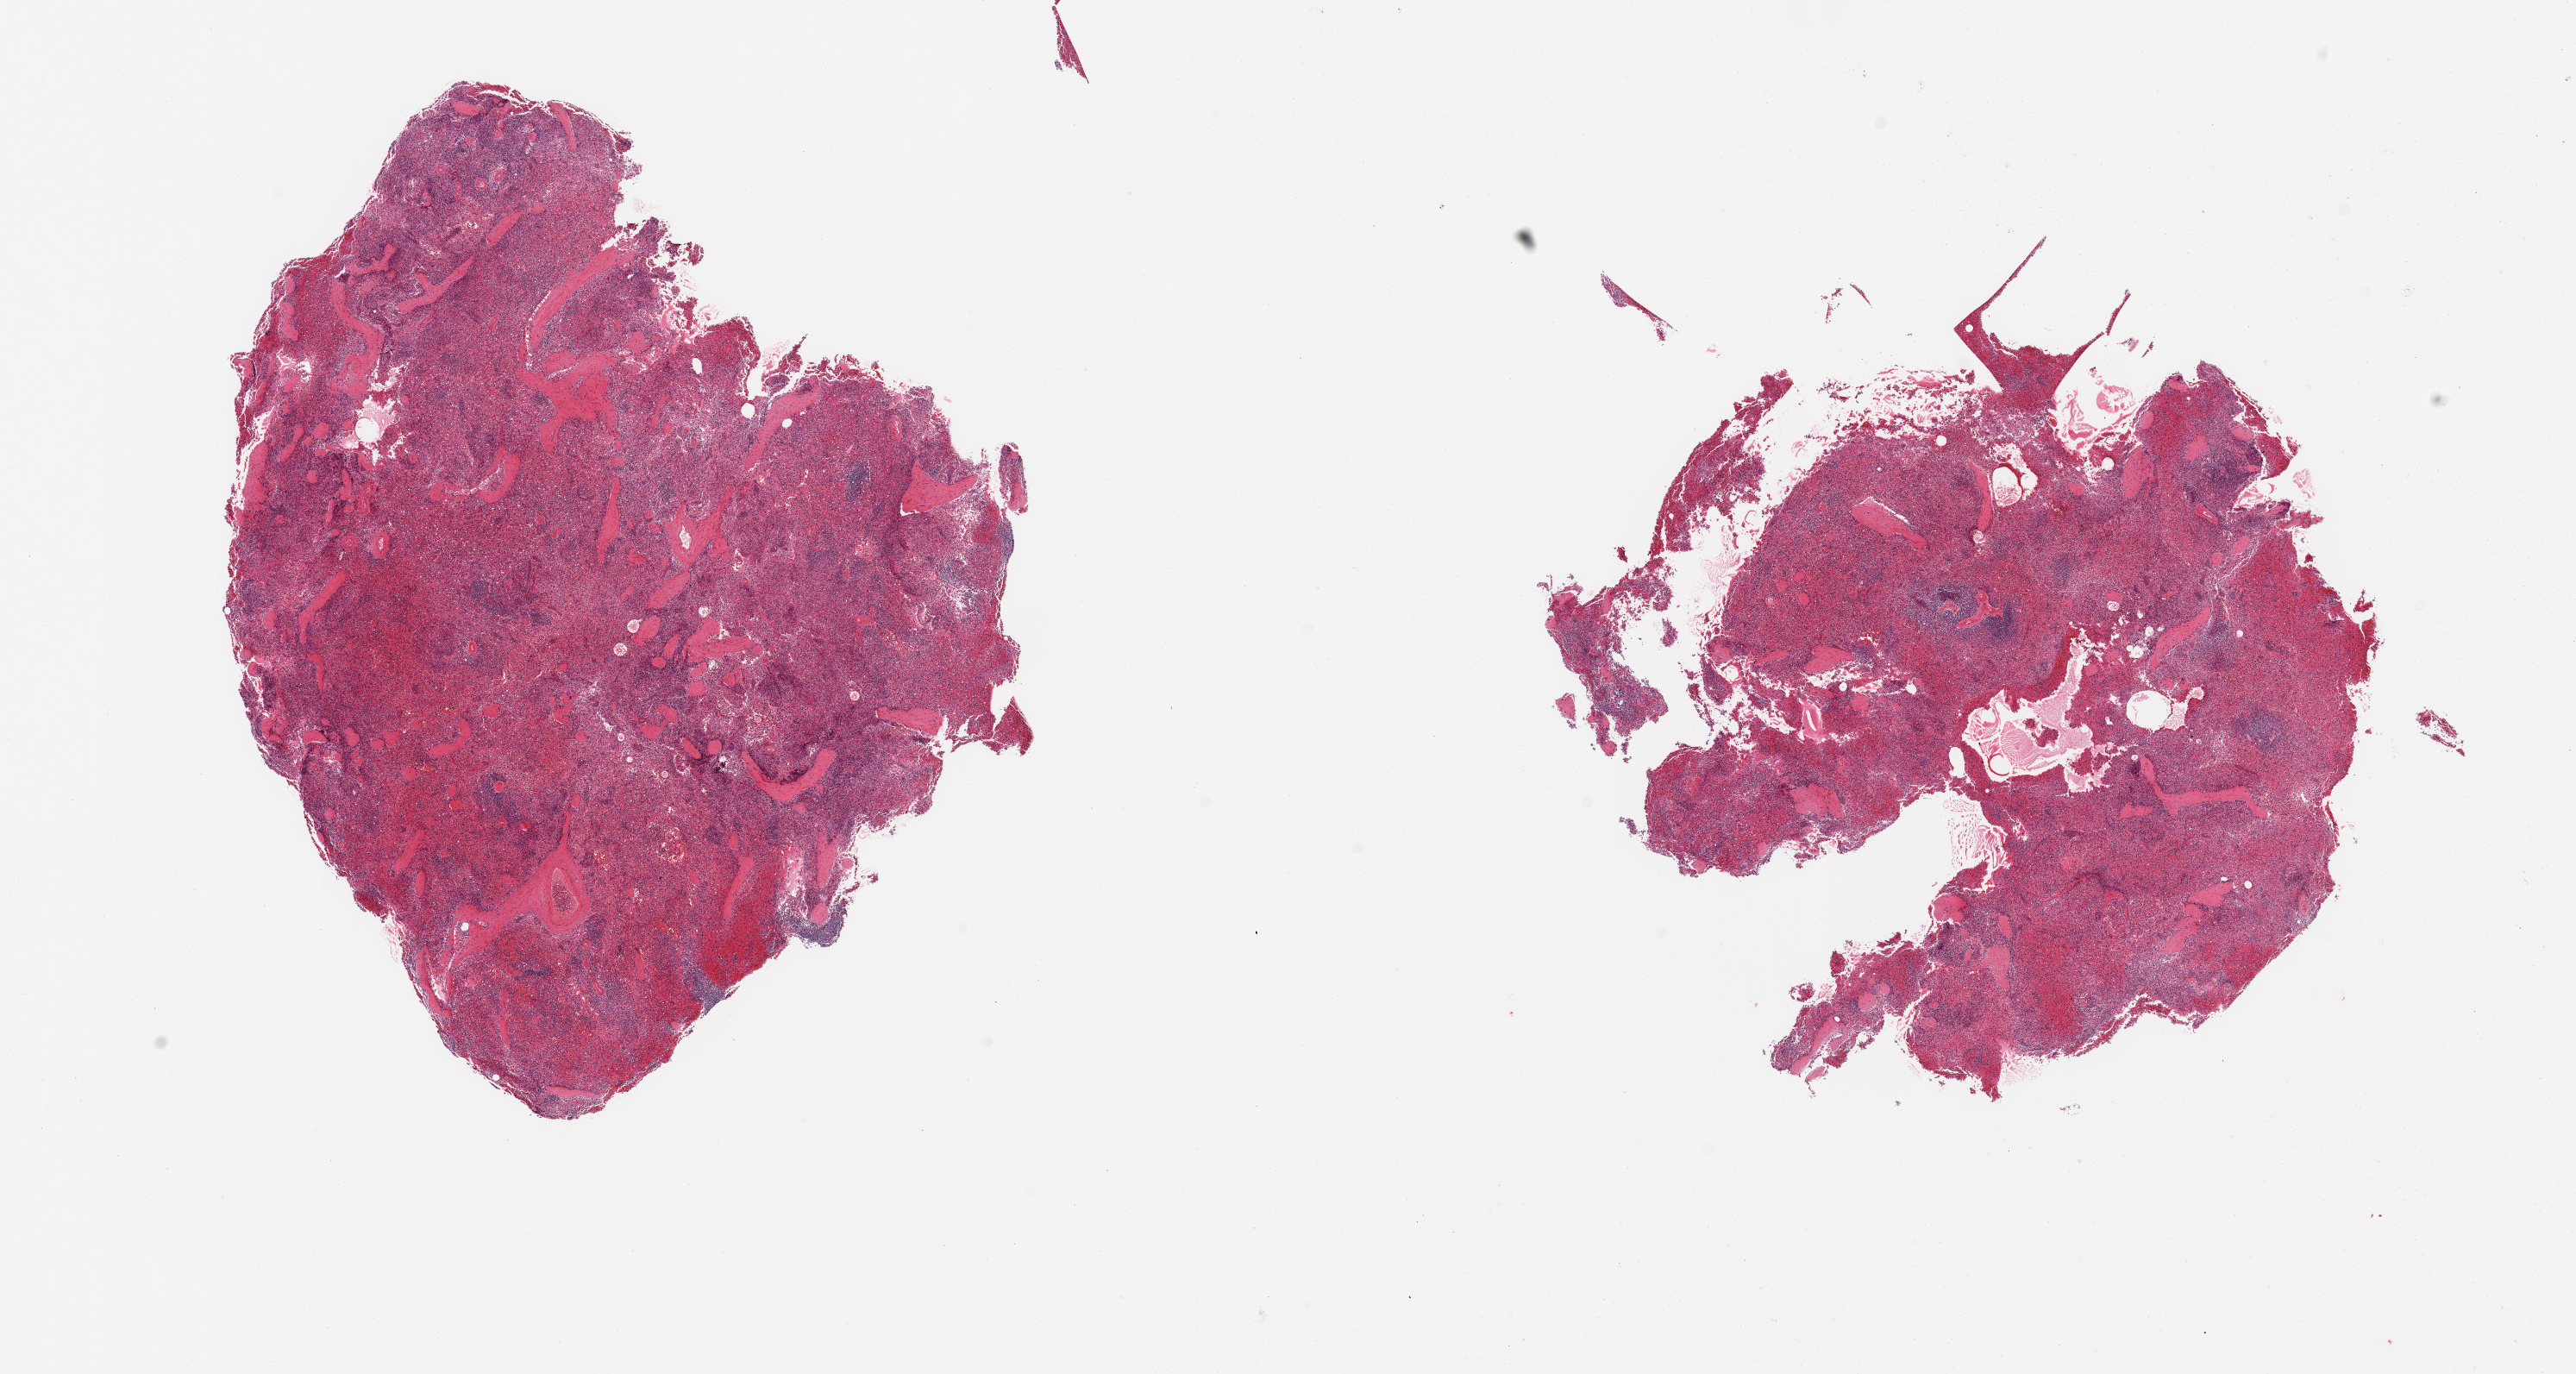
Digitized haematoxylin and eosin-stained section — shown as a low-resolution overview of the whole scanned area (about 23.6 x 12.6 mm, from a 20x scan). PAXgene-fixed, paraffin-embedded tissue. Section of spleen (target tissue). Donor tissue sample. Female donor.
- reviewer comment on this tissue sample: 2 pieces, minimal congestion